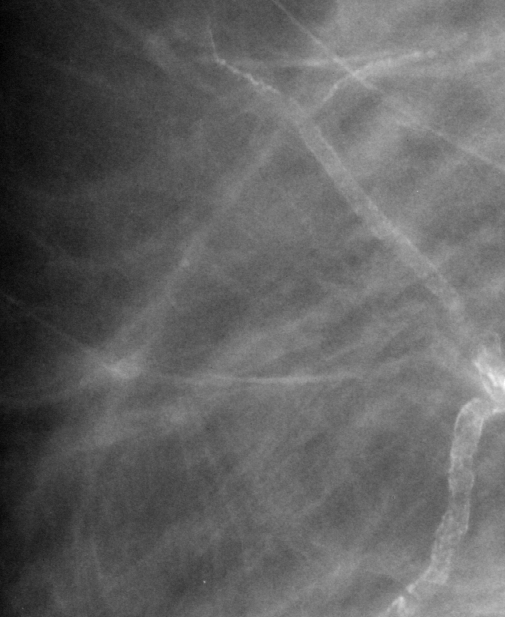
Region of interest cut from a scanned film mammogram (one marked finding), right breast, MLO view, BI-RADS breast density category 2 (scale 1–4).
- Marked abnormality: calcifications, morphology vascular; BI-RADS assessment category 2; benign without callback (not worked up further).